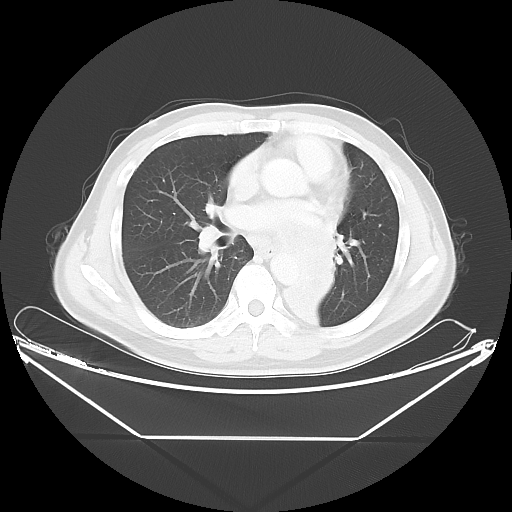
Chest CT, one axial slice. Position 23 of 48 along the scan axis. 120 kVp. Lung window (W 1500 / L -600 HU). 5 mm slice thickness. 512 × 512 image matrix, field of view 438 × 438 mm. Patient: male, 58 years. Case-level facts recorded for this patient, not image findings: clinical TNM (as recorded): T3 N3 M0.
Structures marked on this image (rectangle marked by the reading radiologist):
- lung tumour (recorded histology: squamous cell carcinoma): bounding box [x1, y1, x2, y2] px = [284, 230, 355, 321]